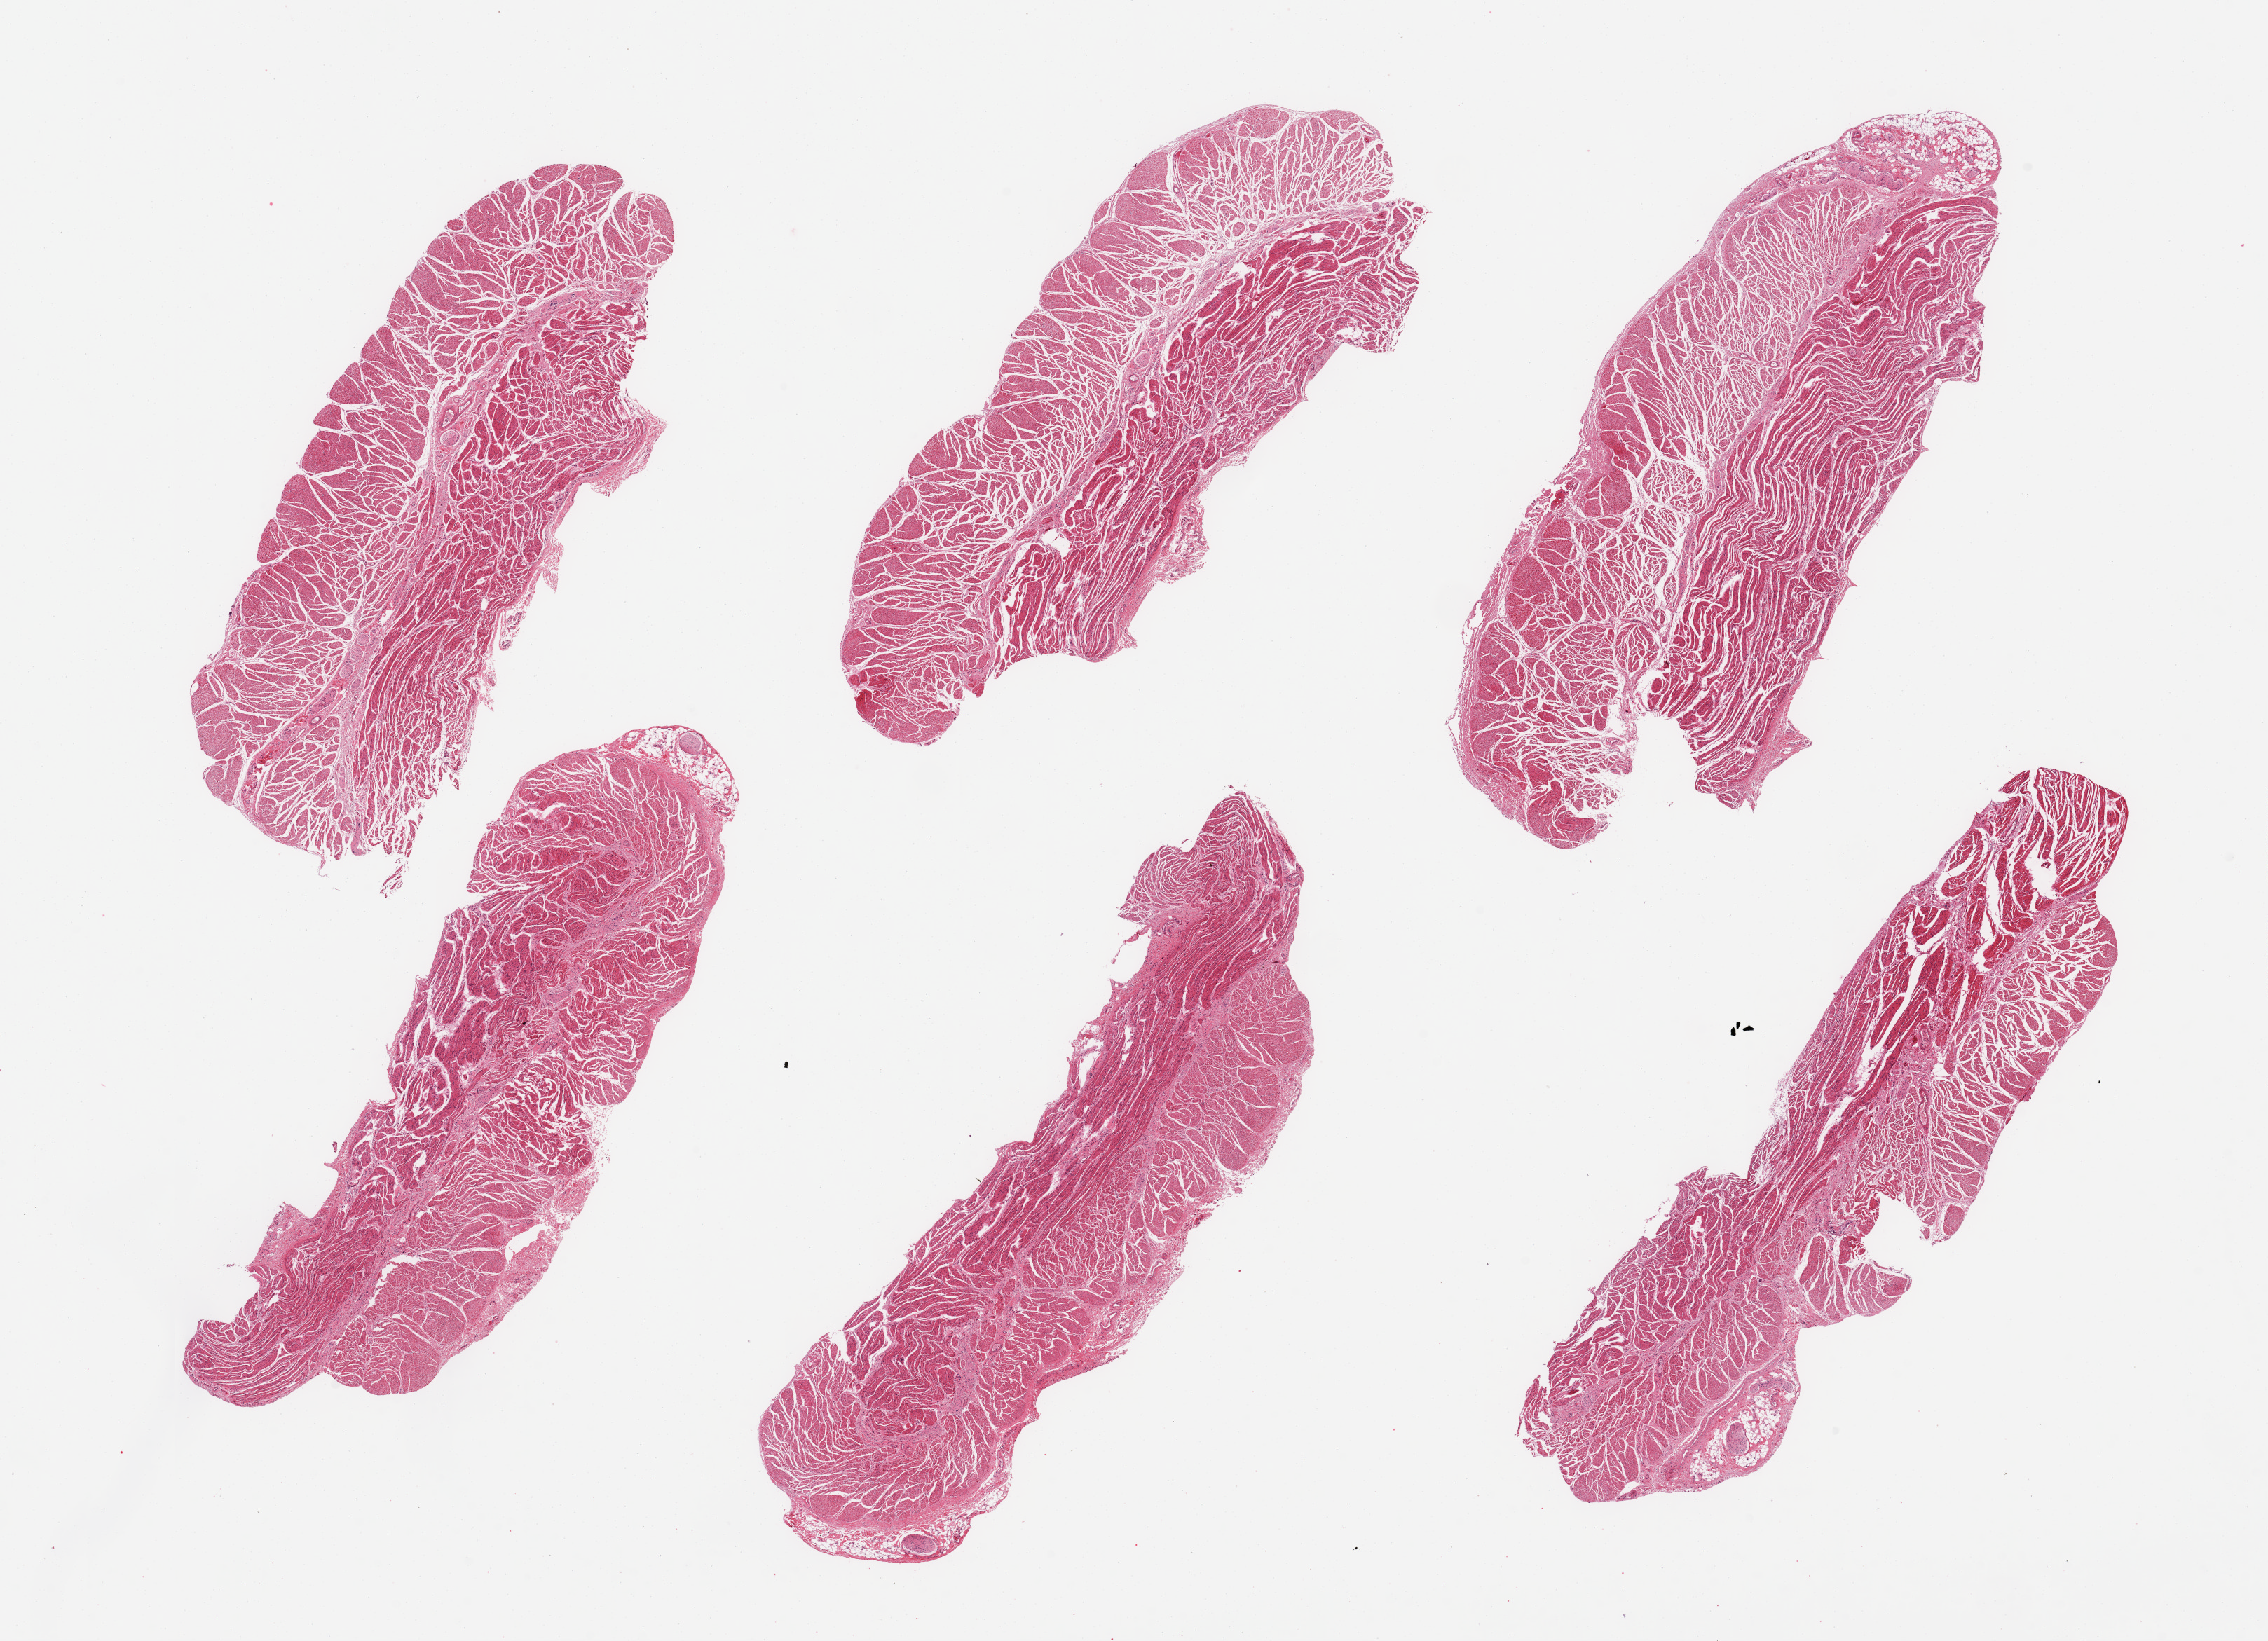
Digitized hematoxylin and eosin (H&E)-stained section, shown as a low-resolution overview of the whole scanned area (about 25.6 x 18.5 mm), PAXgene-fixed, paraffin-embedded tissue, section of gastroesophageal junction (target tissue), donor tissue sample. Male donor.
- reviewer comment on this tissue sample: 6 pieces, confirmed target muscularis